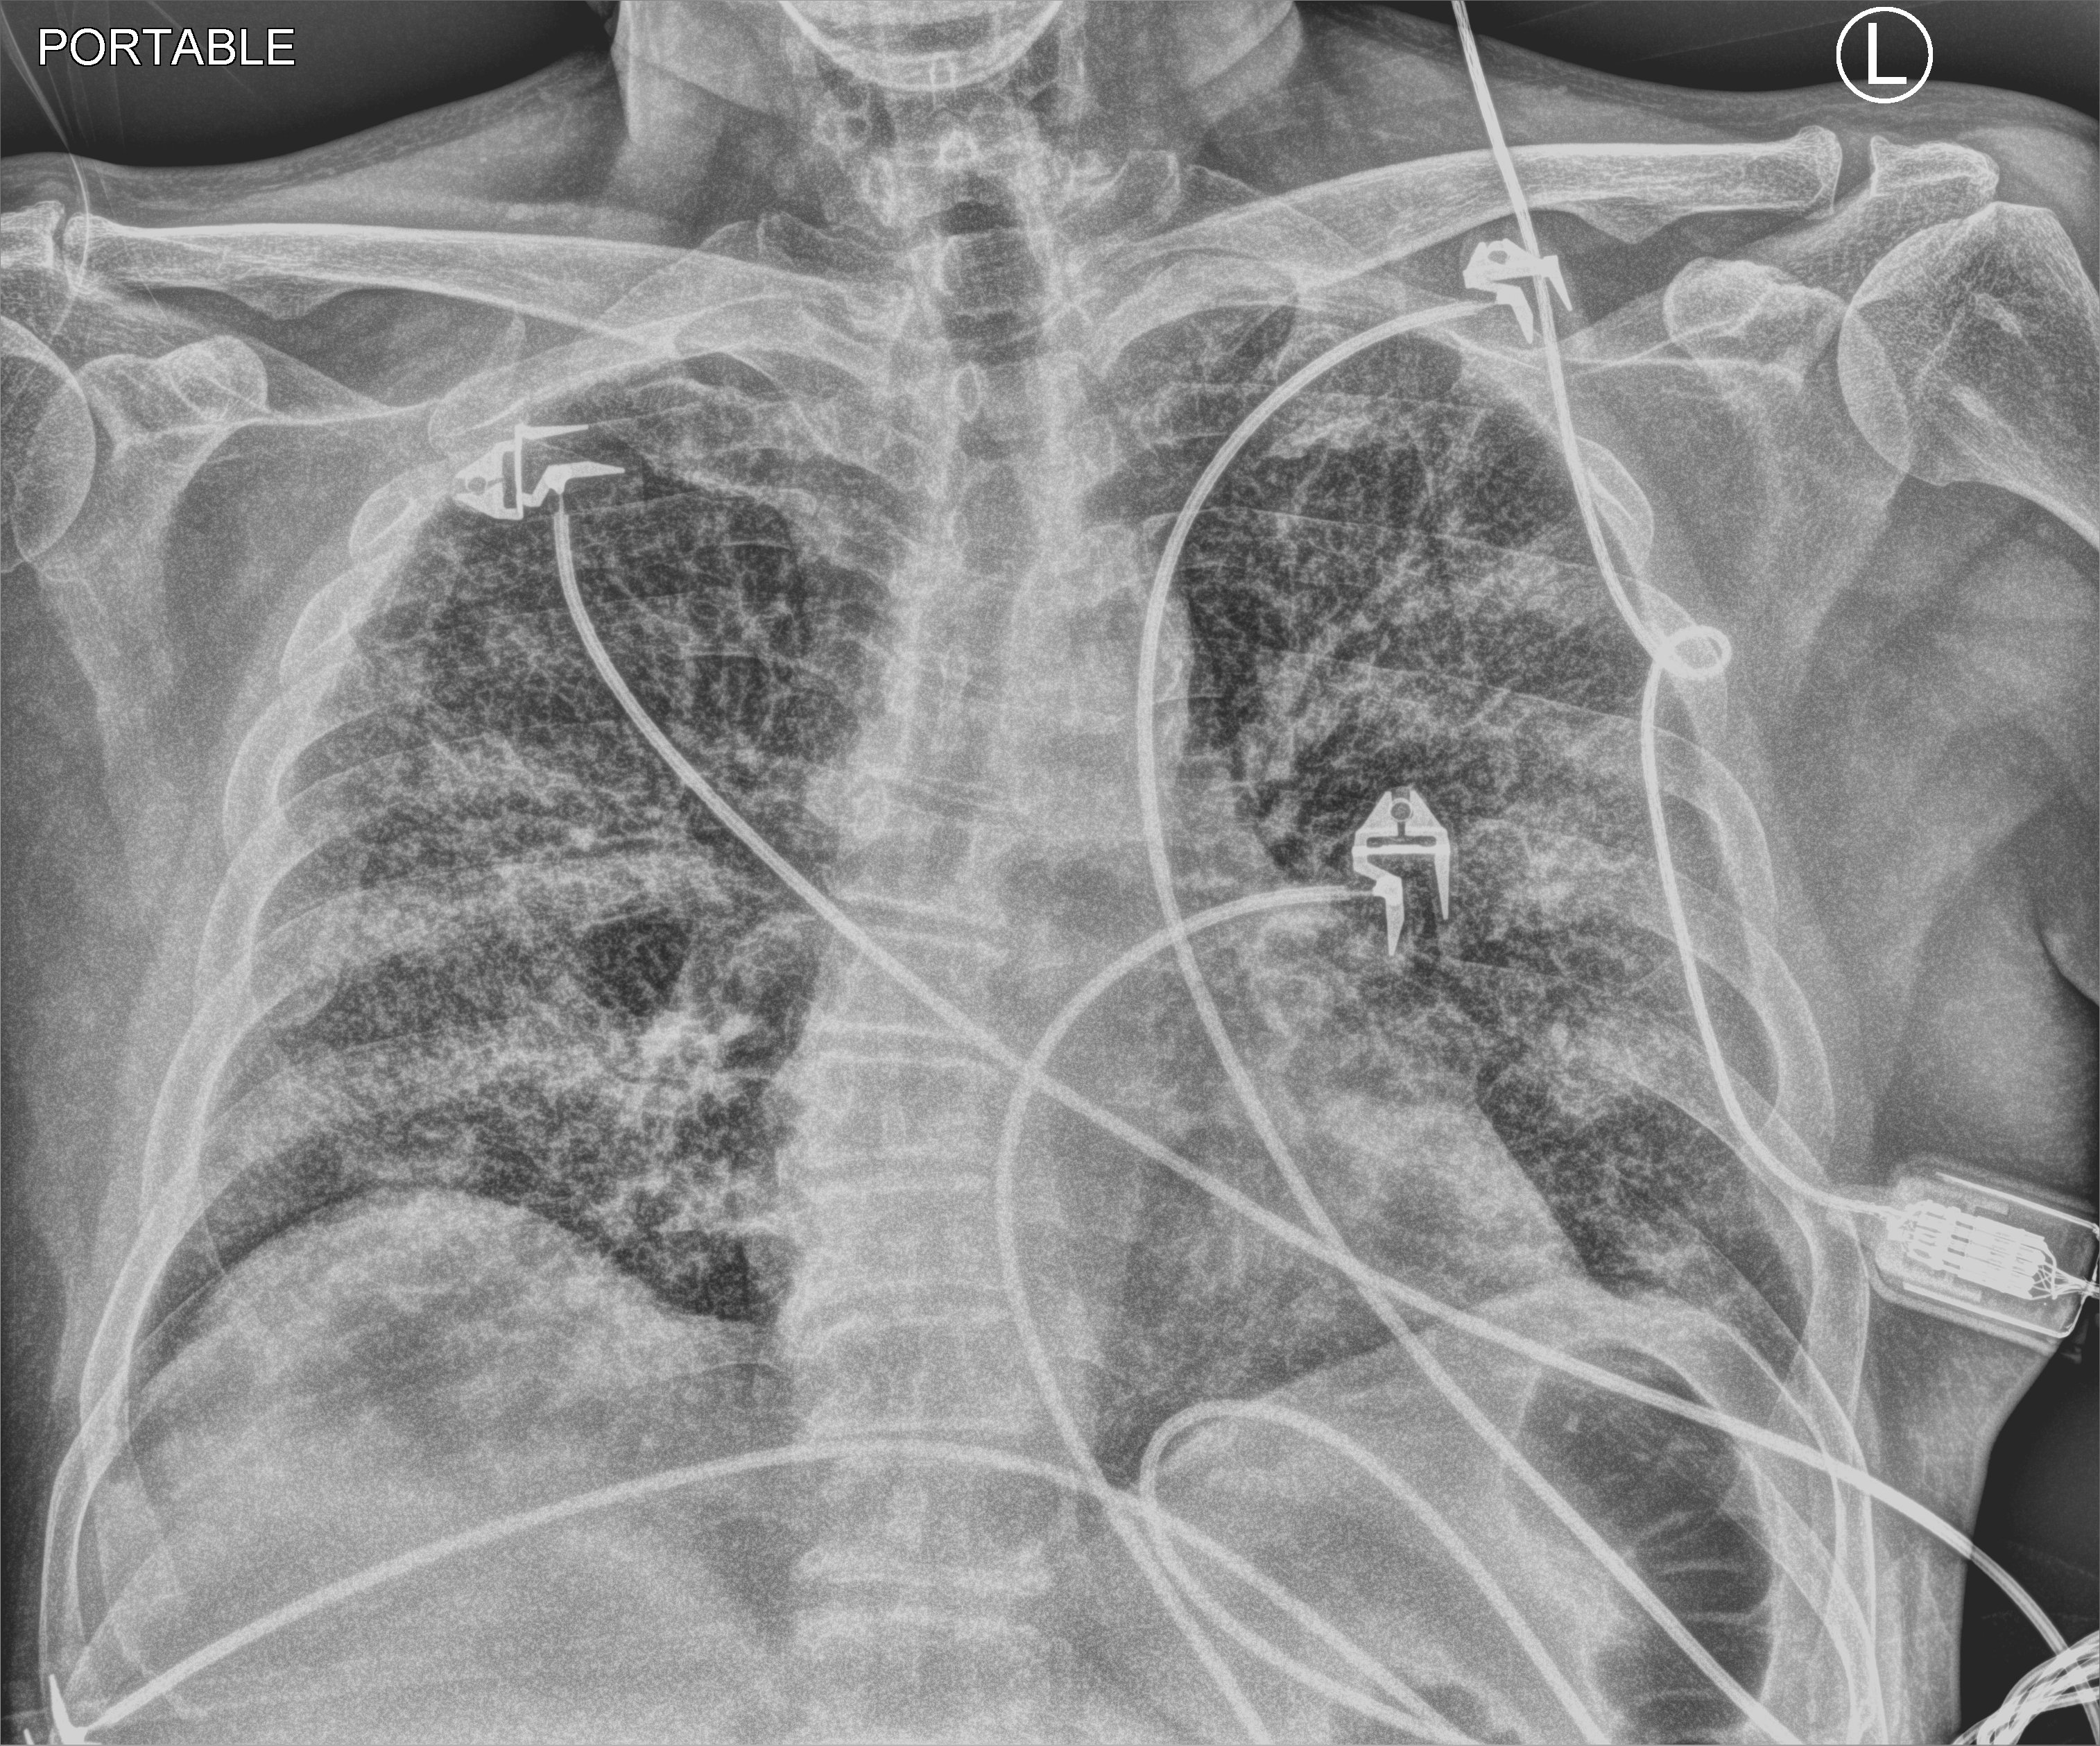
Portable chest radiograph; anteroposterior (AP) projection. Patient hospitalised with COVID-19; male, aged 18–59 years.
Hospital-stay facts (about this admission, not read from this image; timing relative to this image not recorded): hypertension (admission record): yes.